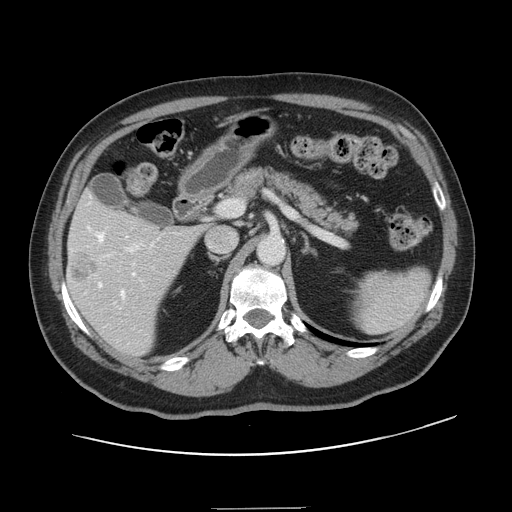
Contrast-enhanced abdominal CT, one axial slice; slice 80 of 143 in the series (ordered by position); 120 kVp; intravenous contrast given; soft-tissue window (W 400 / L 40 HU); 512 × 512 image matrix, field of view 402 × 402 mm. Male patient, age 62 years. Case-level facts recorded for this patient, not image findings: diagnosis: colorectal cancer liver metastases, imaged before liver resection; multiple liver metastases: yes; largest metastasis: 2.7 cm; disease in both lobes: no.
Structures marked on this image (outlined manually by an expert reader):
- hepatic veins: box from (x=88, y=196) to (x=135, y=297) px
- liver: (x=67, y=195)–(x=201, y=356)
- planned liver remnant (the part of the liver to remain after resection): (x=72, y=195)–(x=138, y=233)
- portal vein (with intrahepatic branches): (x=114, y=245)–(x=139, y=304)
- liver metastasis: (x=73, y=255)–(x=97, y=282)